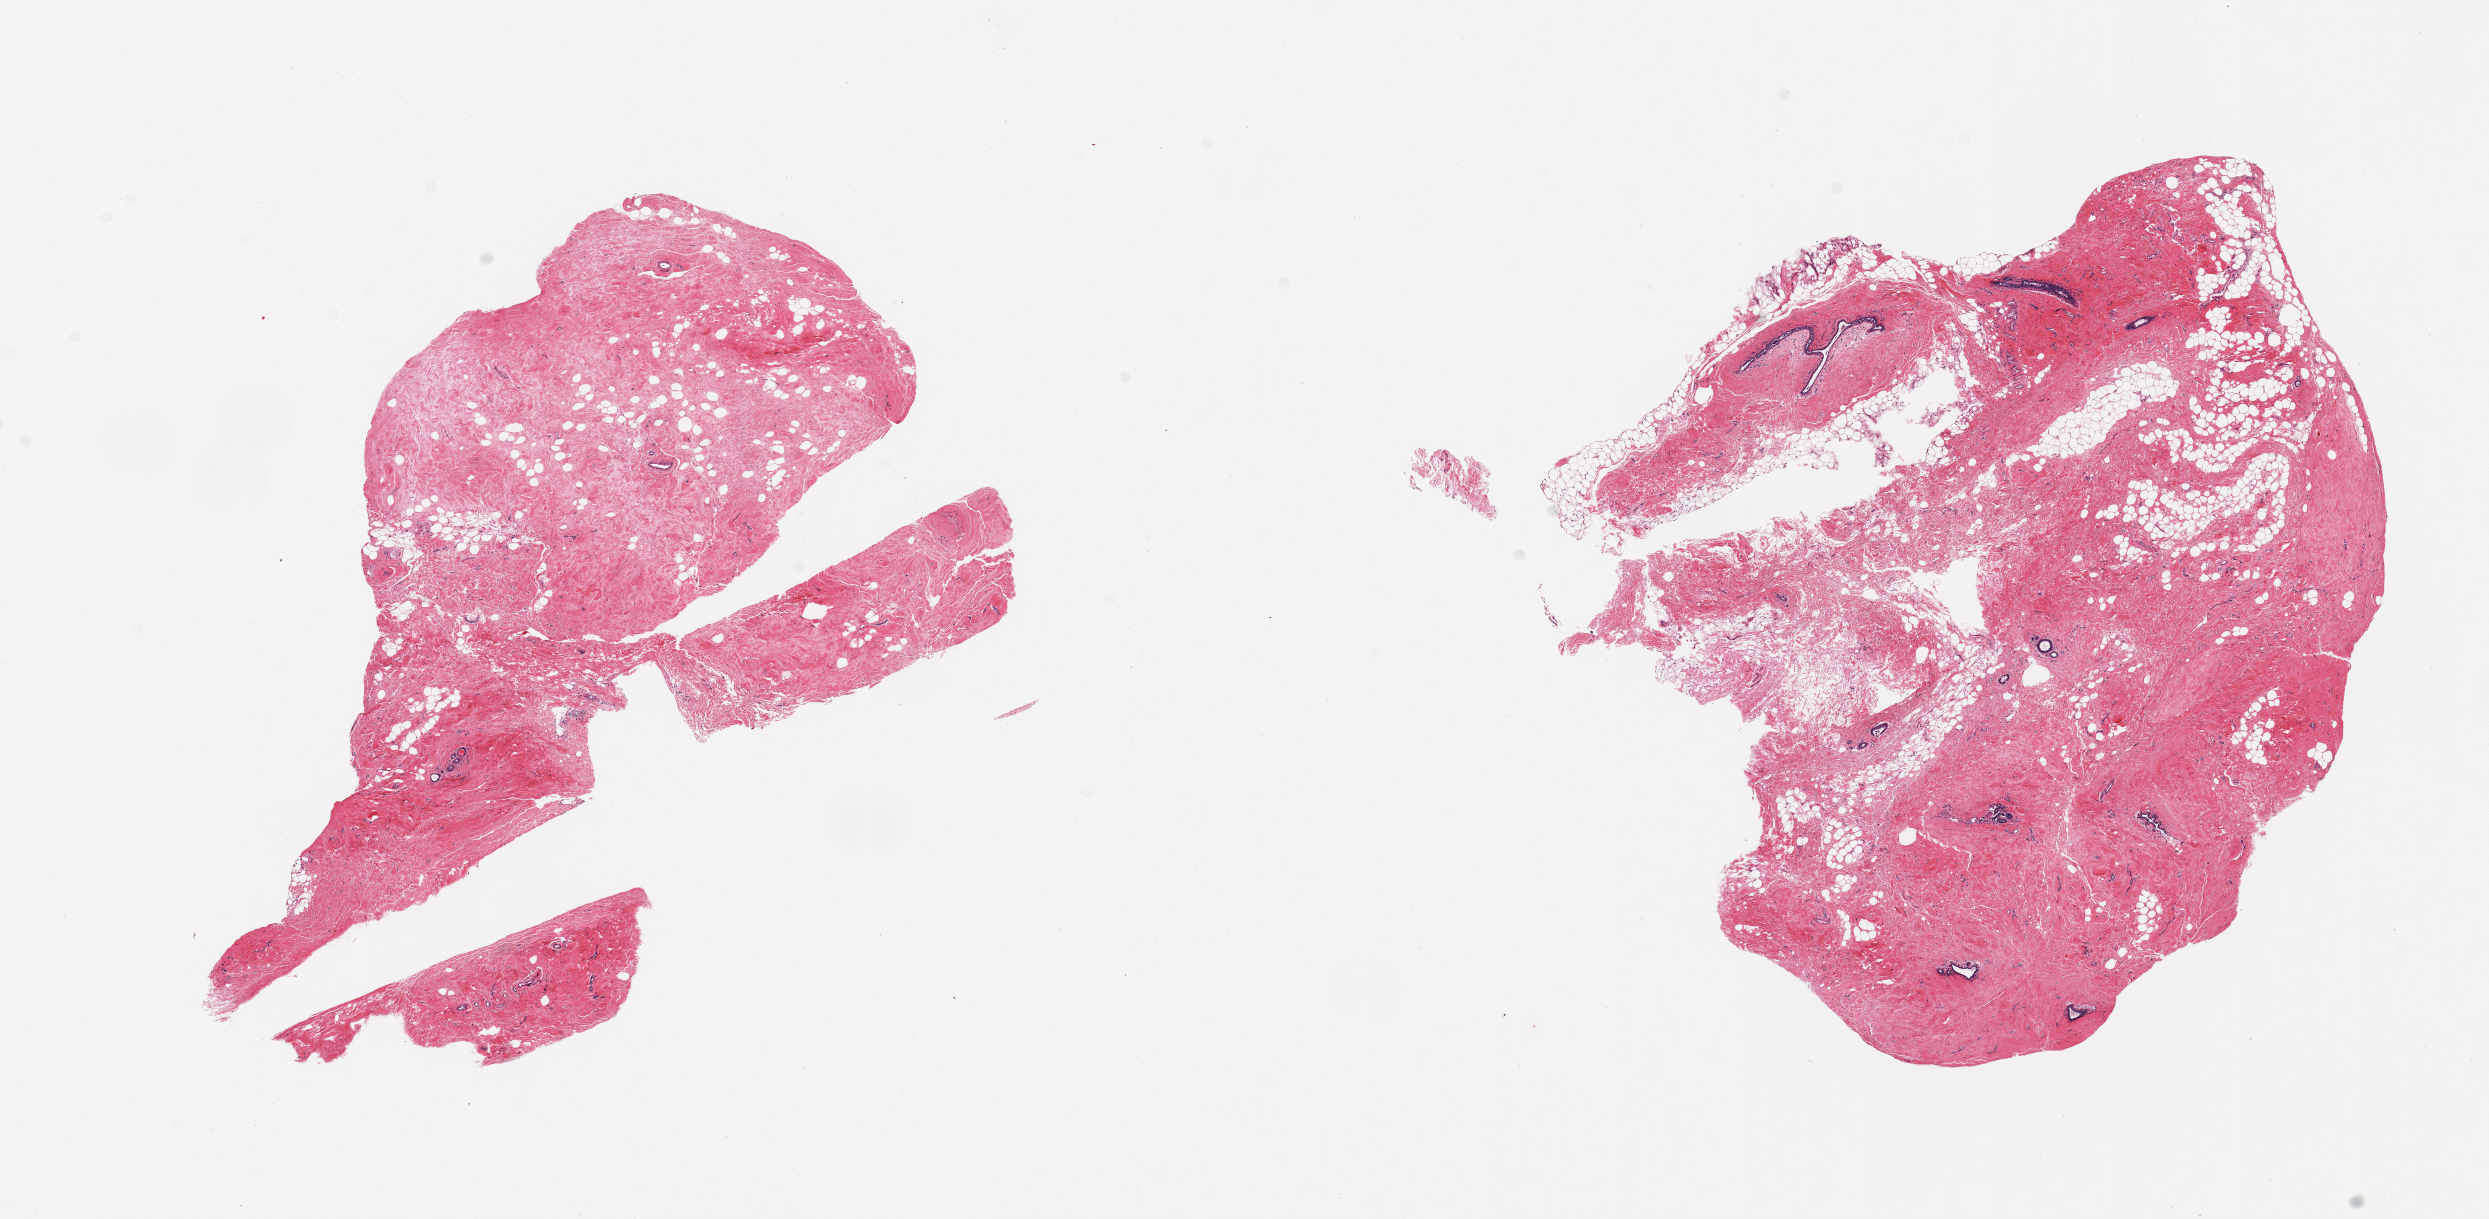
Digitized hematoxylin and eosin (H&E)-stained section, brightfield, low-resolution overview of the scanned area, about 19.7 x 9.6 mm (from a 20x scan), PAXgene-fixed paraffin-embedded (PFPE) section, target tissue: breast, tissue donor sample. Donor sex: female.
Review note (as recorded): 2 pieces, fibrous mastopathy; Inactive ductal elements.